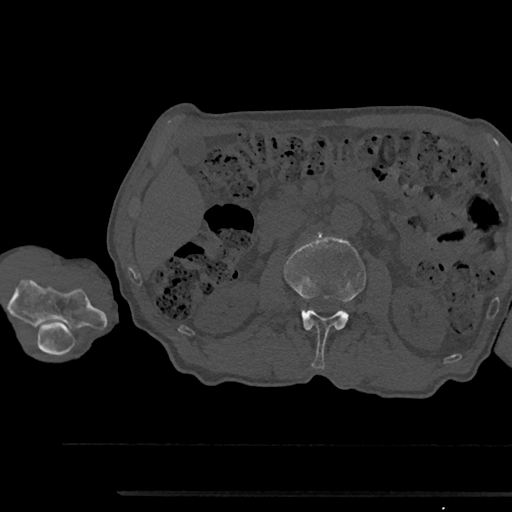
CT including the spine, one axial slice. Position 555 of 797 along the scan axis. 120 kVp. Bone window (W 1800 / L 400 HU). 0.5 mm slice thickness. 512 × 512 image matrix, field of view 367 × 367 mm. Patient: male, 79 years. From the clinical record (not read from this slice): primary cancer: prostate.
Outlined on this slice (semi-automatically segmented with operator editing):
- L2 vertebra: bounding box (x1, y1, x2, y2) in pixels: (284, 233, 366, 369)